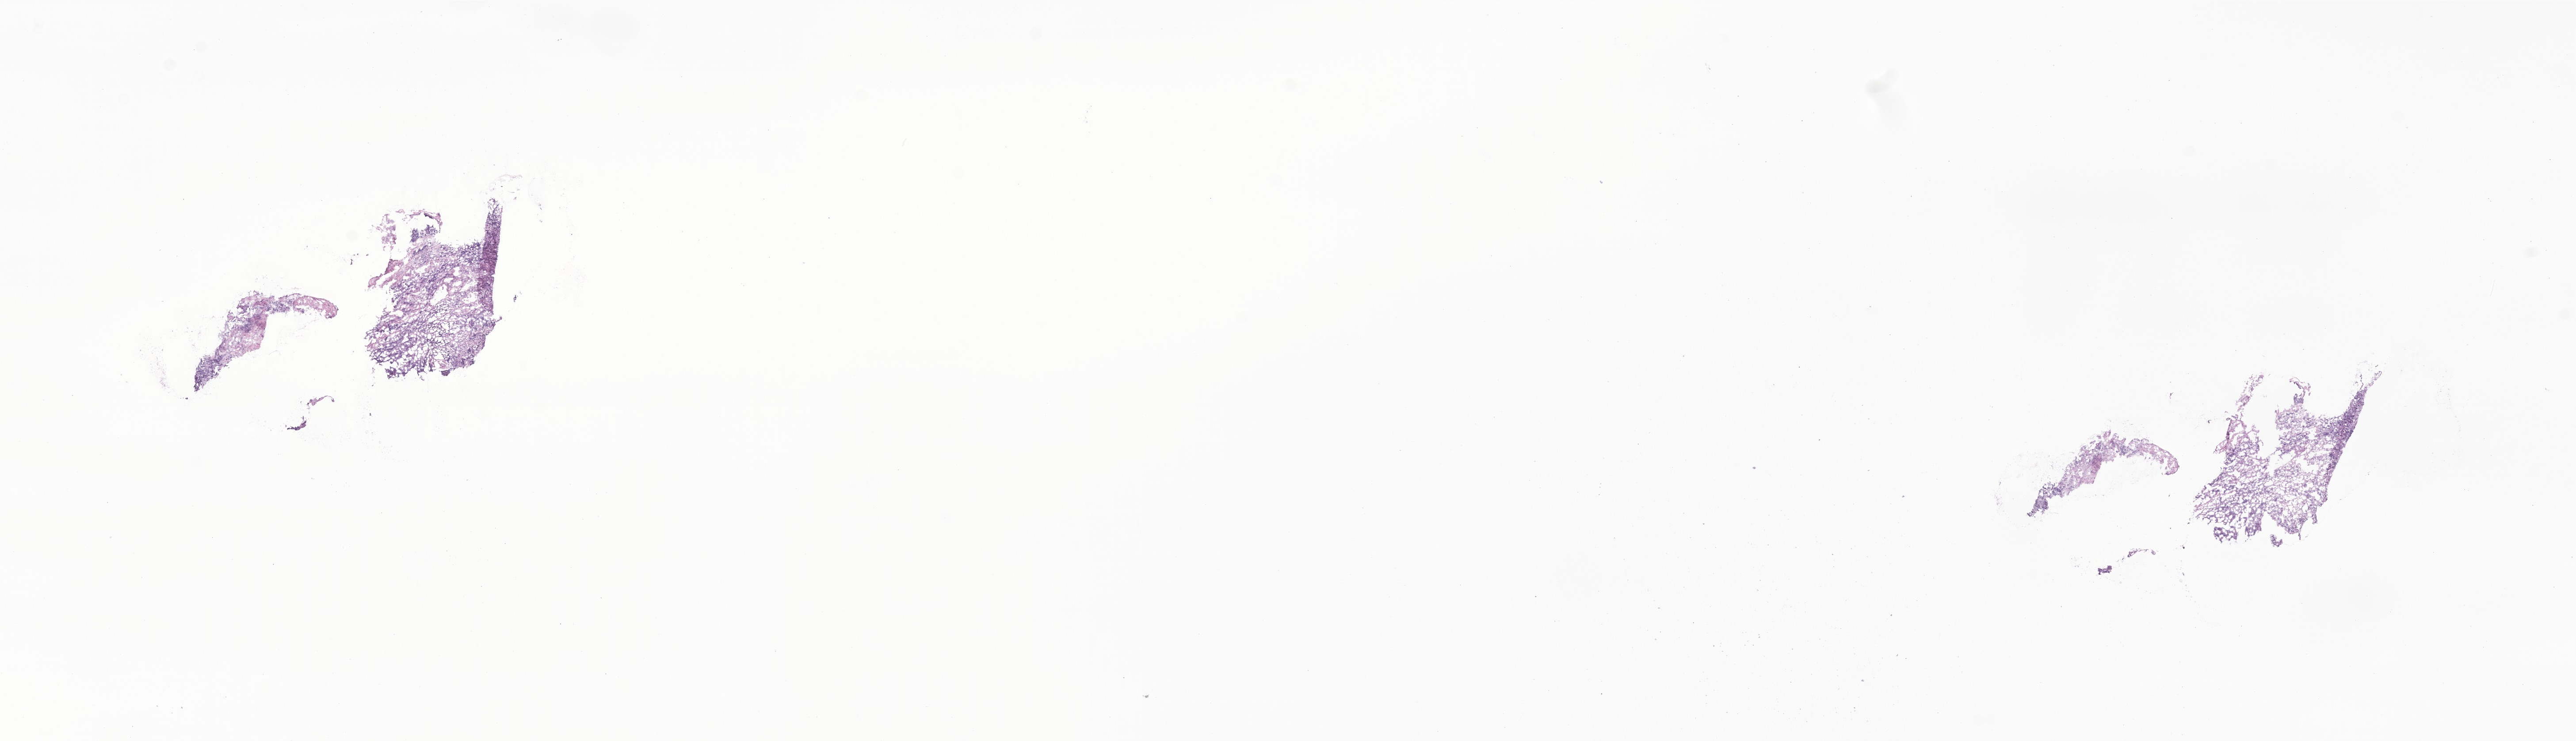
Whole-slide image, haematoxylin and eosin stain of tumor tissue from the retroperitoneum — a low-resolution overview of the entire scanned area, about 24.6 x 7.1 mm; frozen section (OCT-embedded). Male patient, age 273 days.
Recorded diagnosis: Neuroblastoma, NOS.